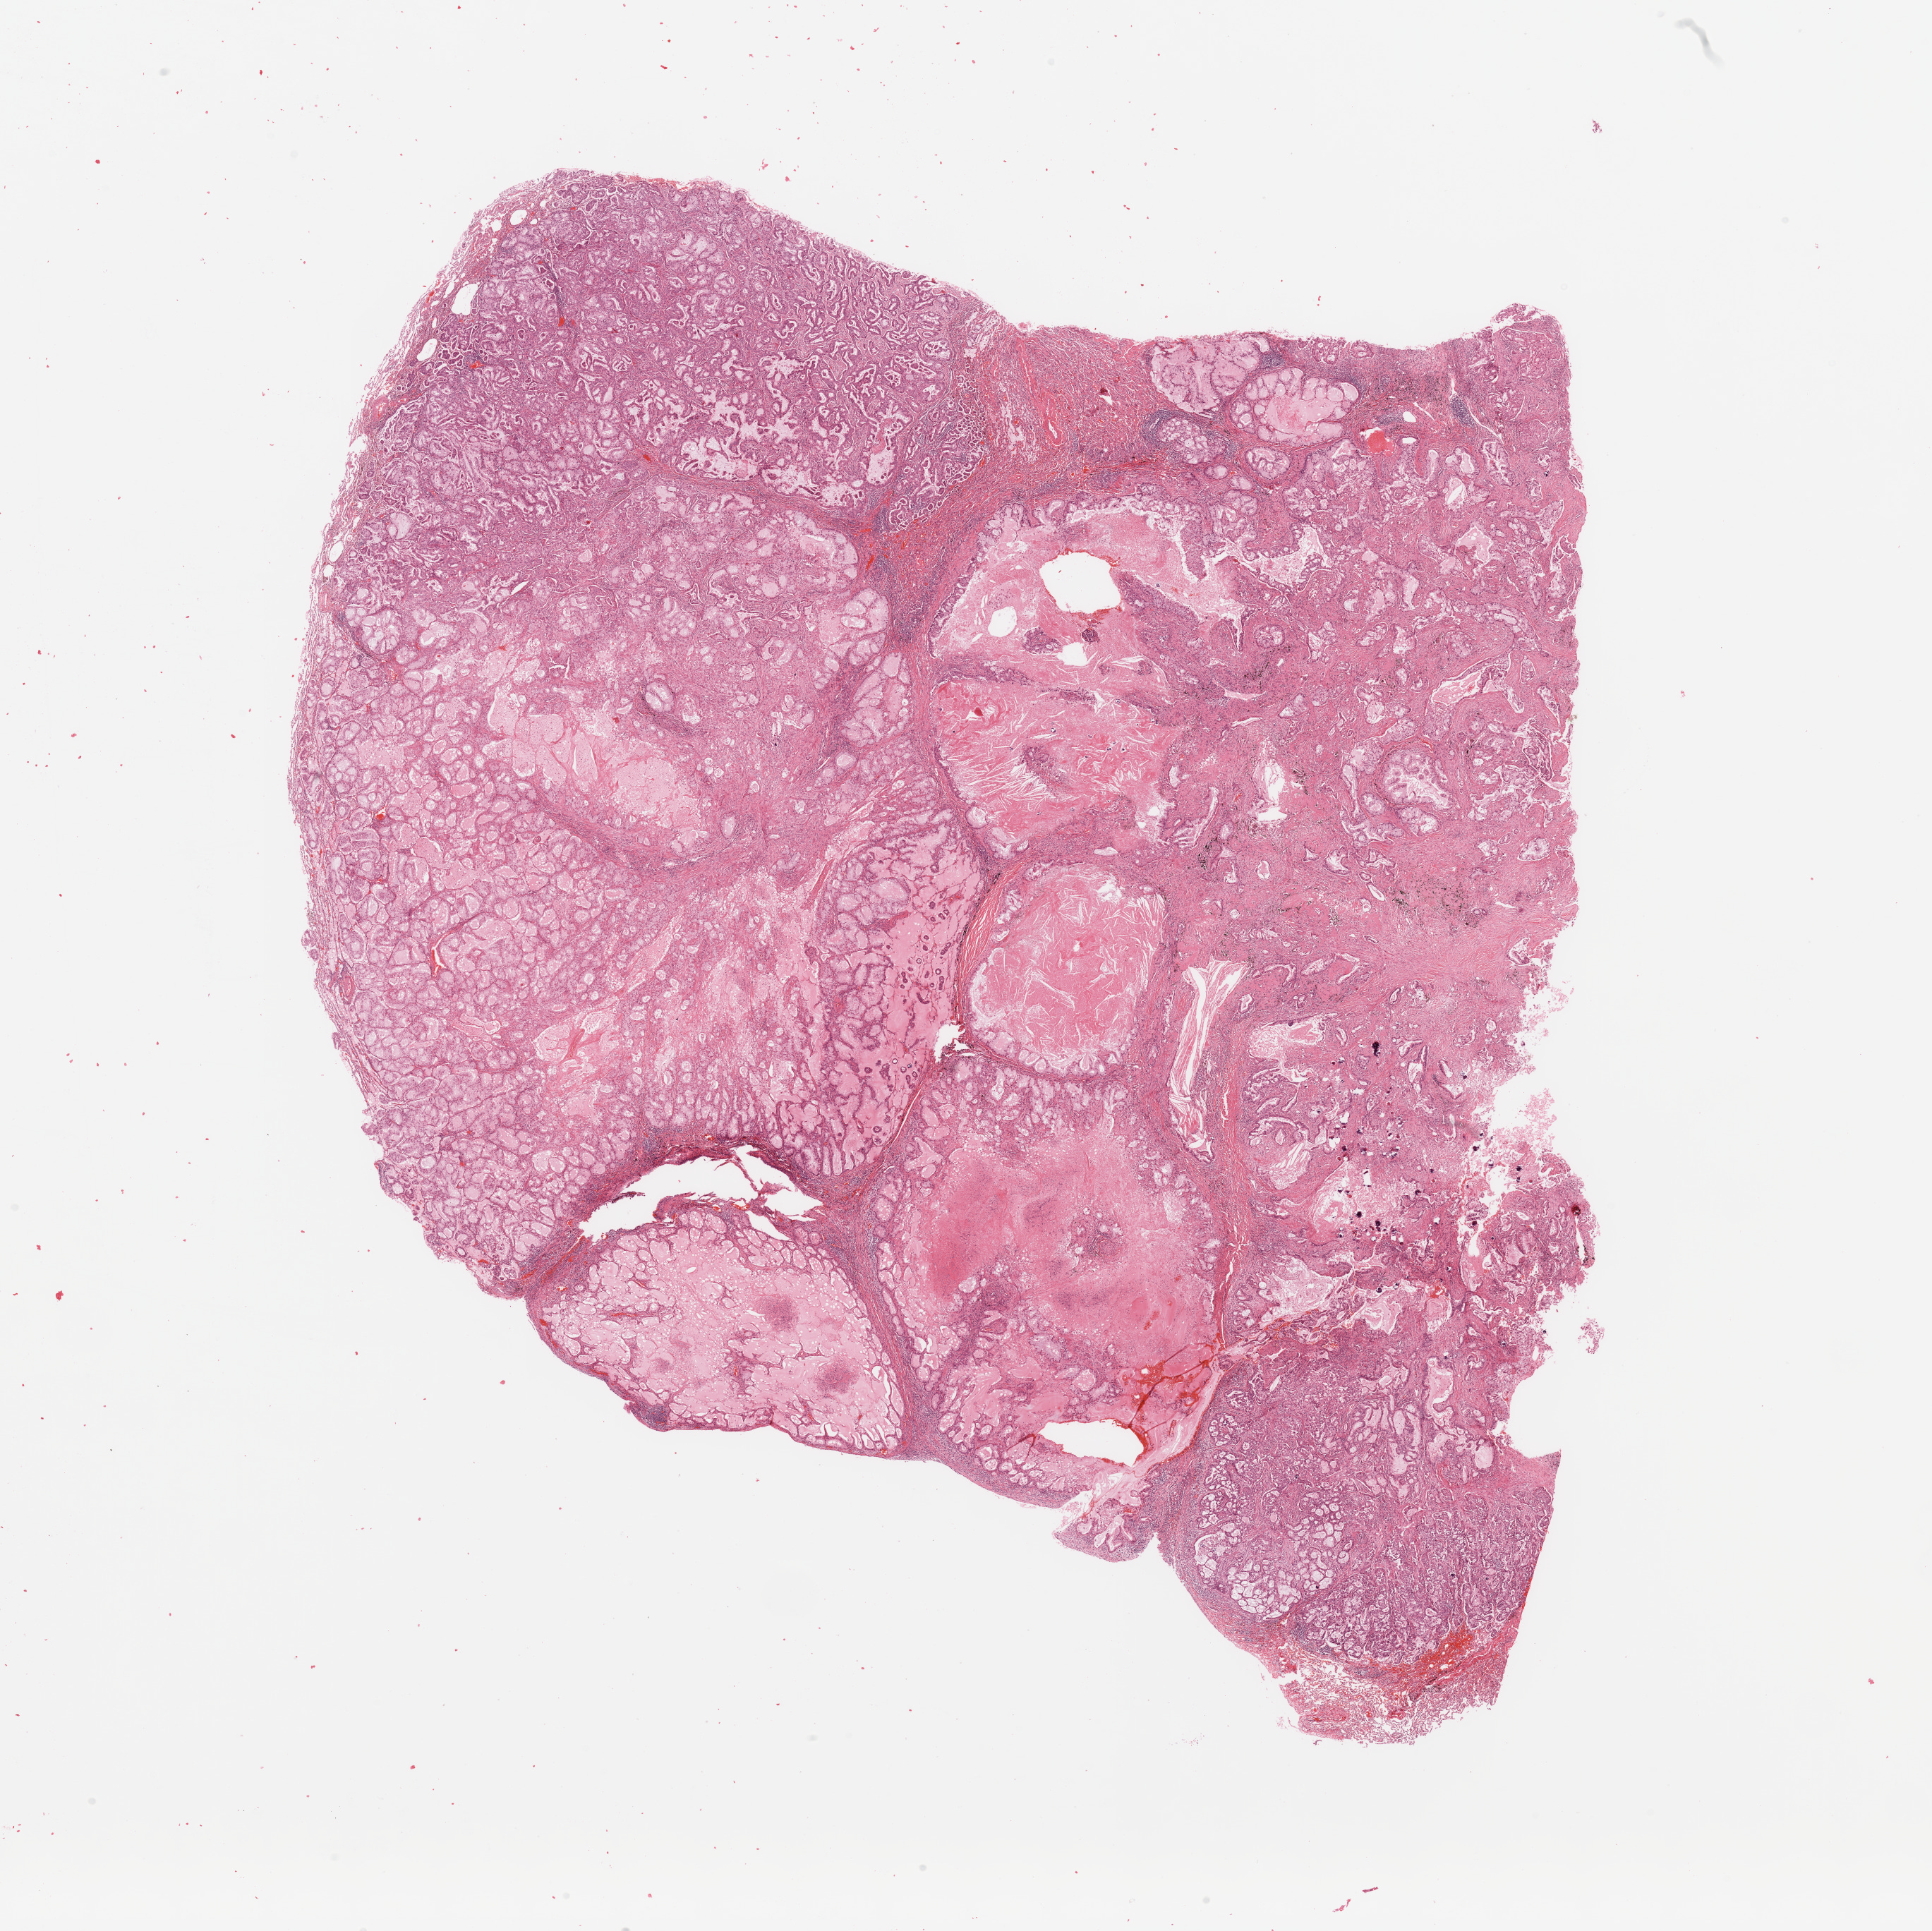
Digitized Hematoxylin and eosin (H&E) stained tissue section (whole slide) — low-resolution overview of the scanned area, about 21.7 x 21.6 mm (acquisition: 20x scan), tumour tissue sample, lung. Male, 48 y/o. Histologic grade: G2 (moderately differentiated).
• histologic diagnosis: Adenocarcinoma, NOS
• AJCC pathologic stage: IIIA